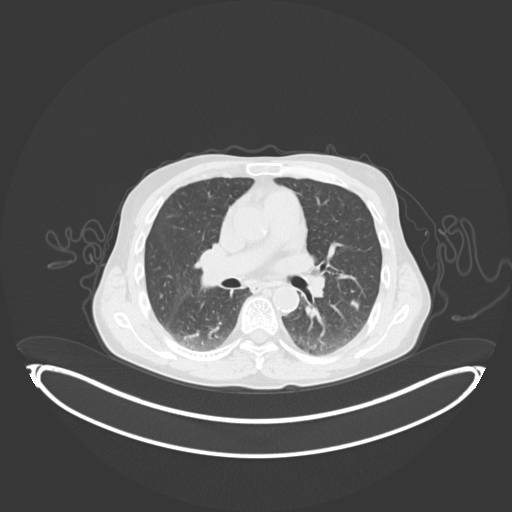
Chest CT, one axial slice. Slice 54 of 102 in the series (ordered by position). 120 kVp. Lung window (W 1500 / L -600 HU). 512 × 512 image matrix, field of view 500 × 500 mm. Patient: male, 58 years. From the clinical record (not read from this slice): clinical TNM (as recorded): T1c N0 M0; histopathological grade: G2.
Annotated regions visible in this slice (bounding box drawn by a radiologist):
- lung tumour (recorded histology: adenocarcinoma): bounding box <349,296,369,312> (left, top, right, bottom; pixels)